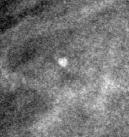
Cropped region of a digitized screen-film mammogram centred on a radiologist-marked abnormality, right breast, MLO view.
- Finding: calcifications, morphology punctate; BI-RADS assessment category 2; subtlety rating 3 on a 1 (subtle) to 5 (obvious) scale; benign without callback (not worked up further).